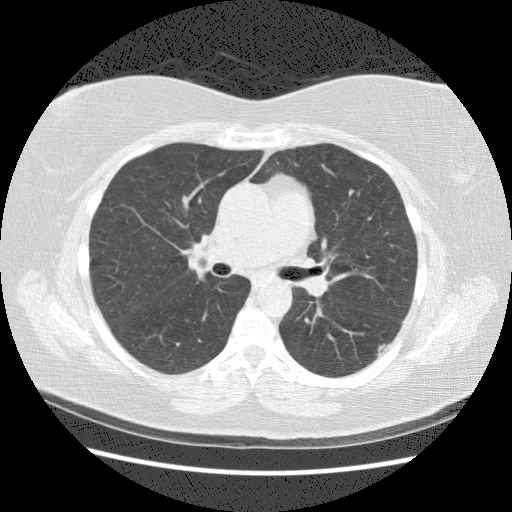
Low-dose screening chest CT, axial slice, second annual screen, lung window (W 1500 / L -600 HU), 2.5 mm slice thickness, slice 82 of 140 in the series. Female, age 57 years at enrolment. Current smoker at enrolment.
- Expert reader's lesion annotation, bounding box (x1, y1, x2, y2) in pixels: (358, 328, 402, 370).
- The exam's reader record, not a measurement of the box and not confirmed to be the same lesion: non-calcified nodule or mass ≥4 mm, left lower lobe, 19 × 9 mm, poorly defined margins, mixed attenuation, pre-existing on the prior screen: yes; interval growth: yes.
- Participant outcome: lung cancer diagnosed 560 days after this screen — squamous cell carcinoma, NOS, left lower lobe, poorly differentiated (G3), stage IB (AJCC 6th edition), 40 mm at pathology.